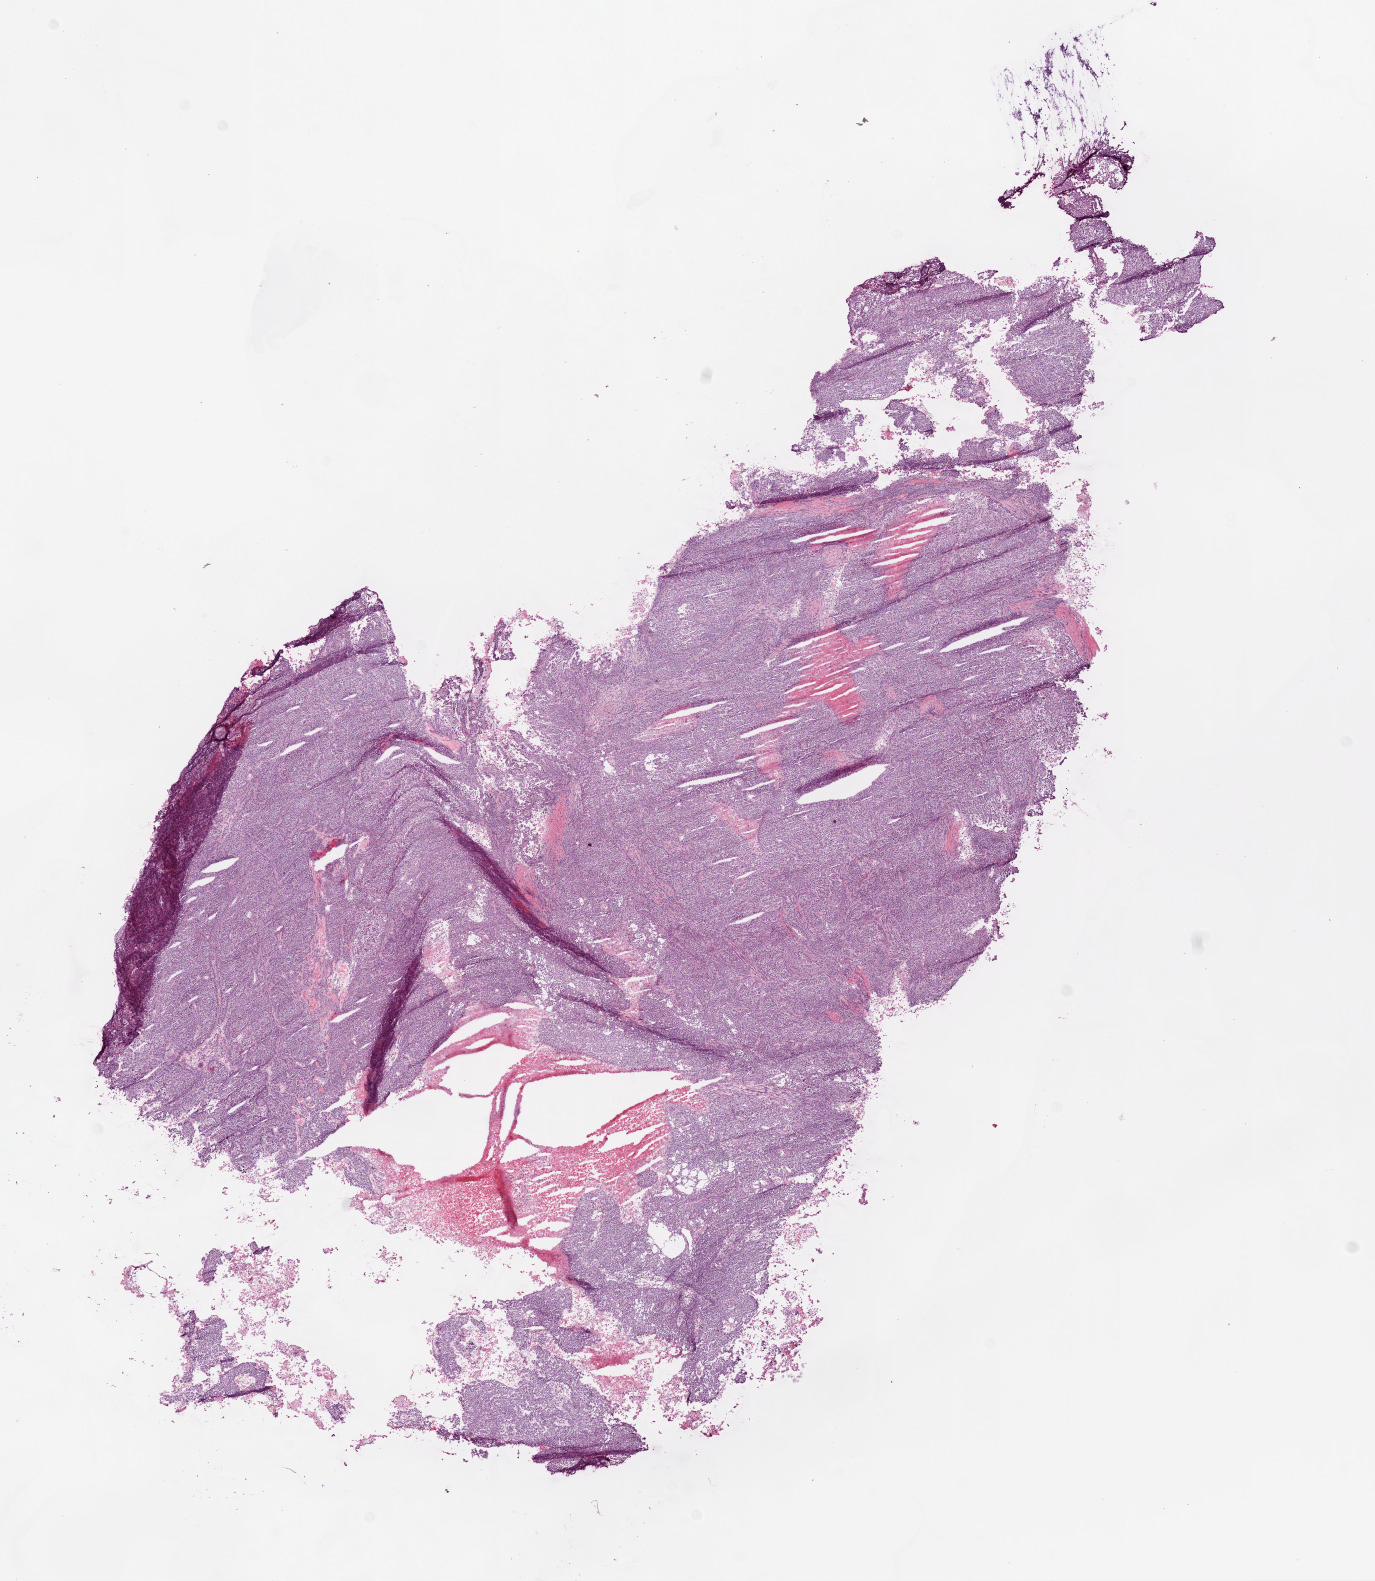
Whole-slide histology image, H&E — whole scanned area (about 11.0 x 12.7 mm, from a 20x scan) shown as a low-resolution overview; frozen section from the bottom of the tissue portion; sample: primary tumour, ovary. Patient: female, age at initial diagnosis 69 years. Histologic grade: G3 (poorly differentiated). Slide review estimates, as recorded: tumour cells 85%, tumour nuclei 85%, normal cells 0%, stromal cells 5%, necrosis 10%. Inflammatory infiltration, as recorded: lymphocyte infiltration 10%.
• laterality: bilateral
• pathologic diagnosis: Serous cystadenocarcinoma, NOS
• FIGO stage: IIIC